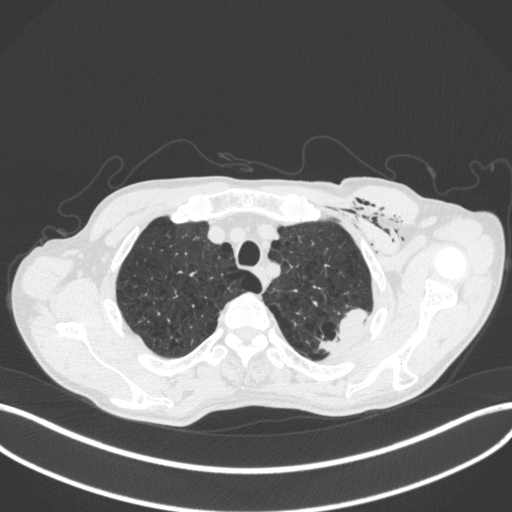
Chest CT, one axial slice; position 350 of 416 along the scan axis; 120 kVp; lung window (W 1500 / L -600 HU); 512 × 512 image matrix, field of view 400 × 400 mm. Patient: male, 58 years. From the clinical record (not read from this slice): clinical TNM (as recorded): T3 N0 M0.
Annotated regions visible in this slice (rectangle marked by the reading radiologist):
- lung tumour (recorded histology: adenocarcinoma): bounding box [x1, y1, x2, y2] px = [315, 303, 371, 357]